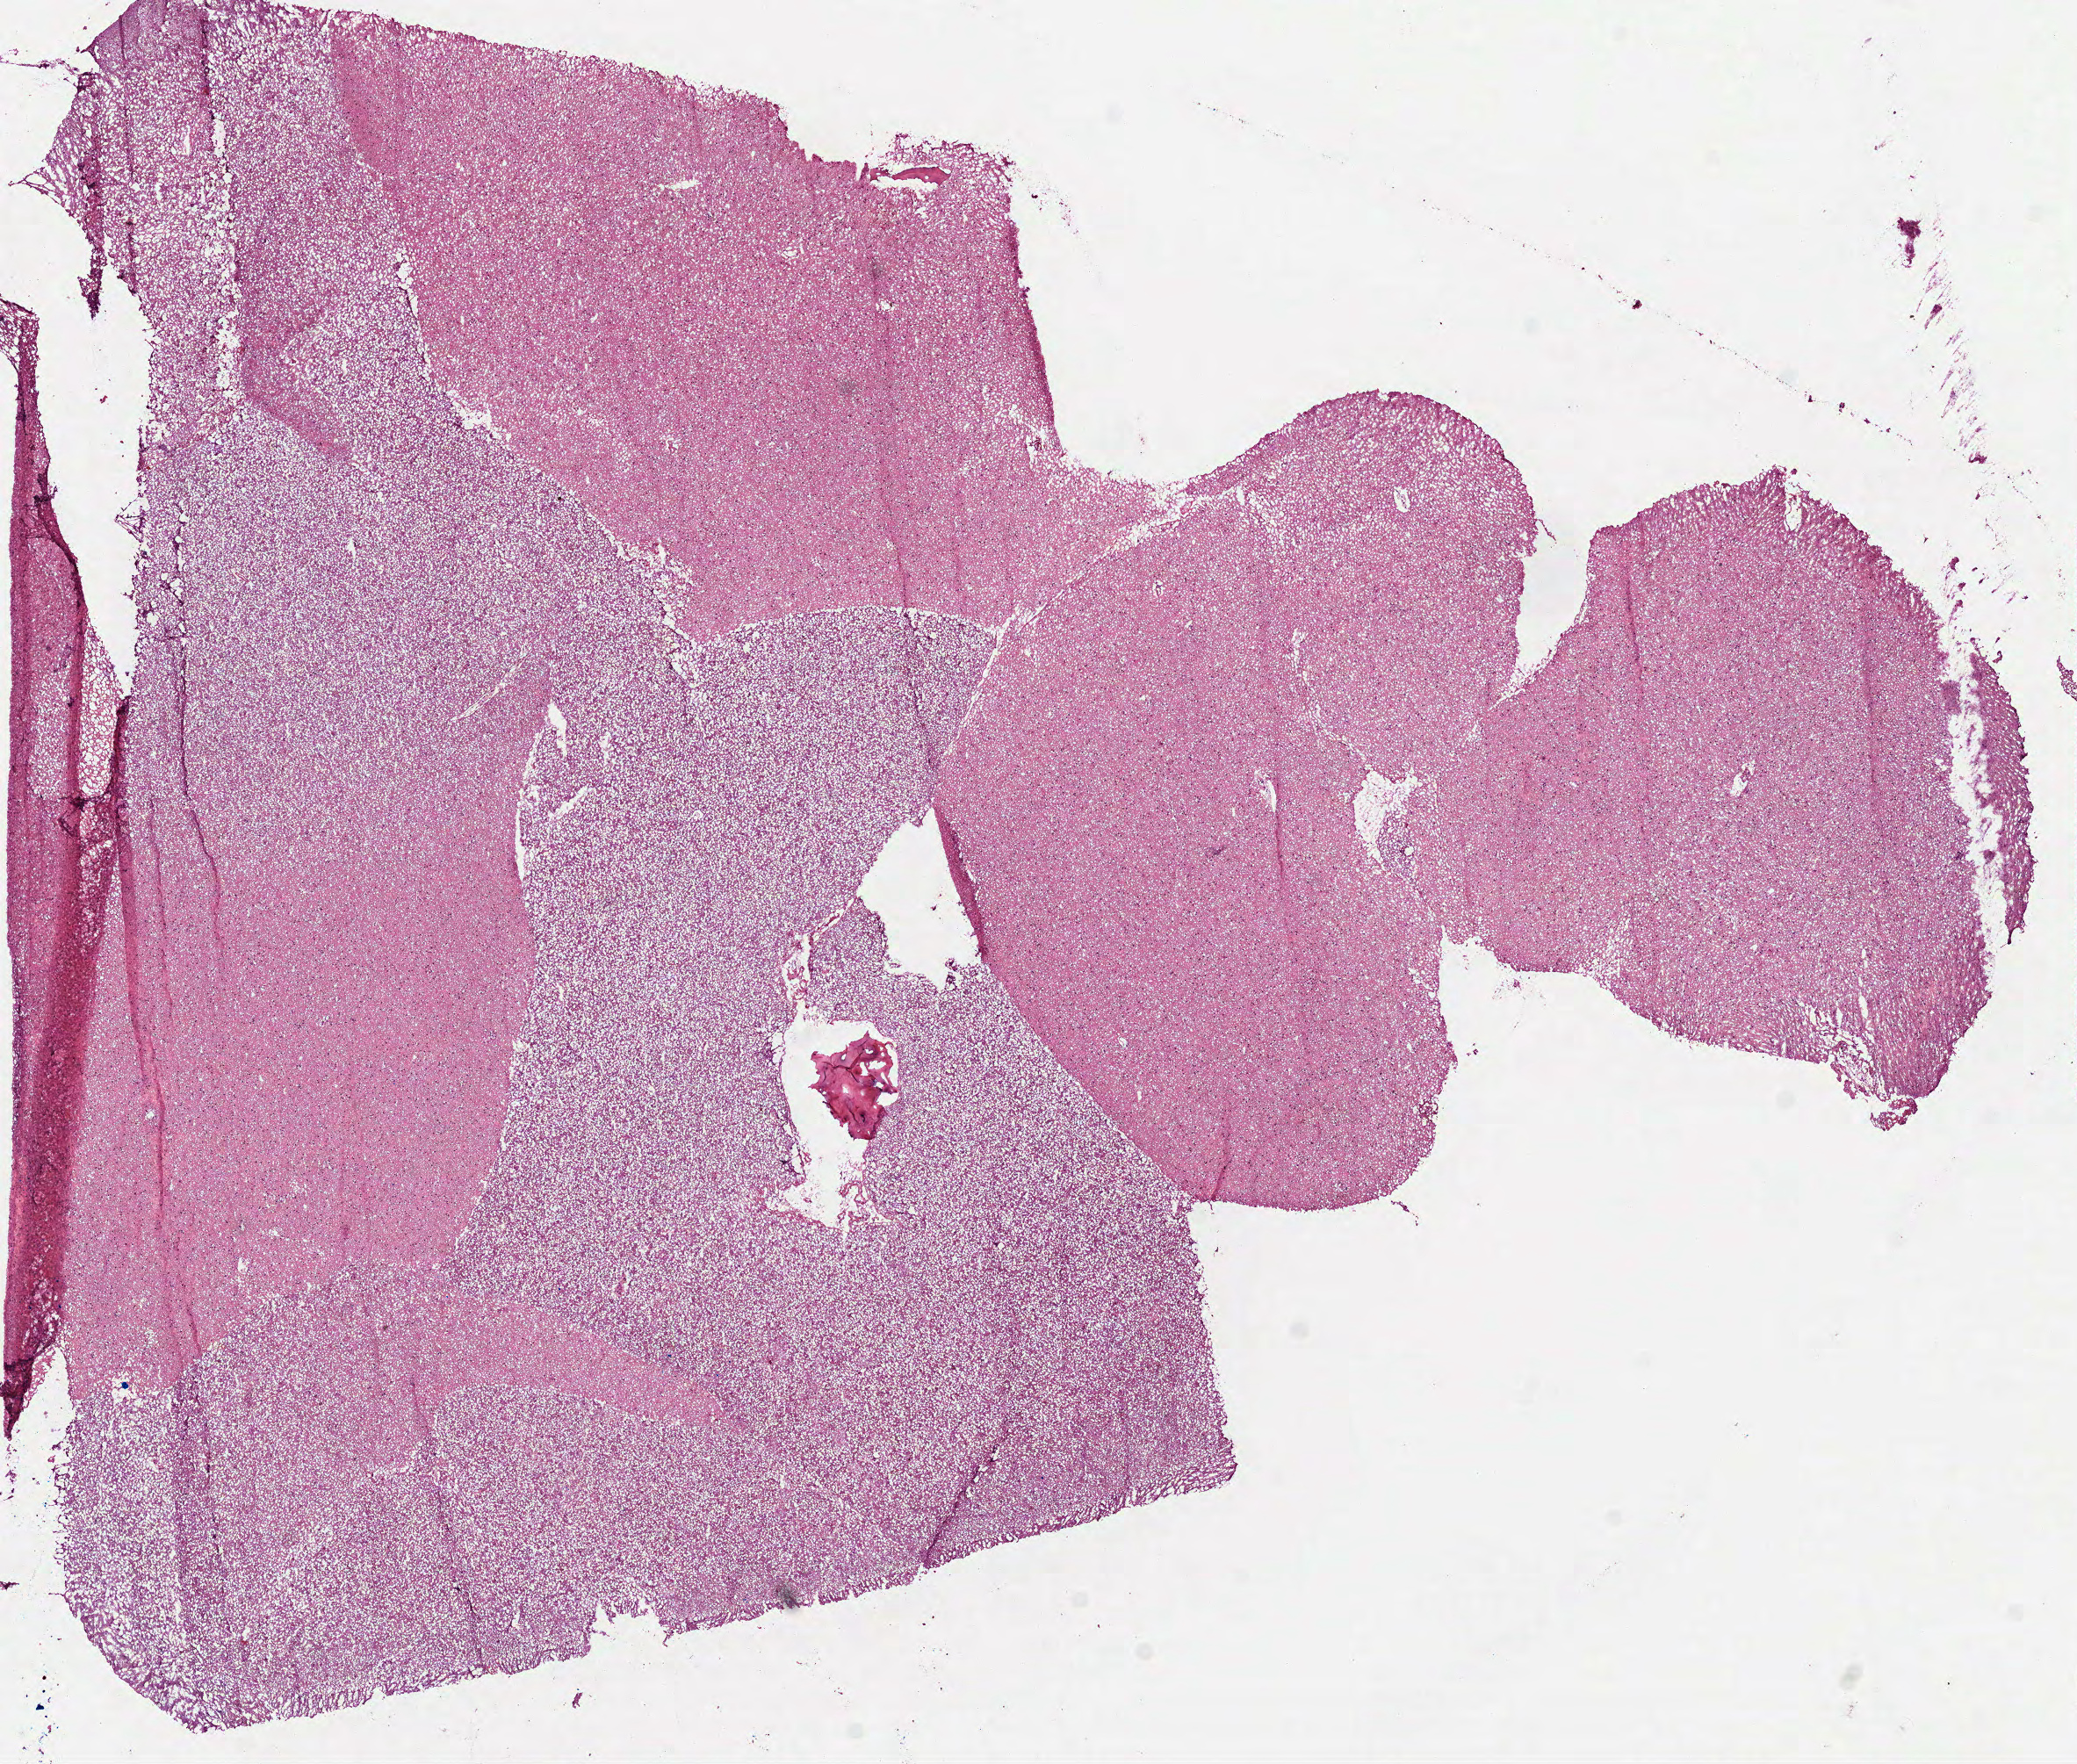
Digitized H&E tissue section (whole slide) — shown as a low-resolution overview of the whole scanned area (about 9.5 x 8.1 mm), frozen section from the top of the tissue portion, brain, solid tissue normal (non-tumour tissue) sample. Male patient; age at initial diagnosis 67 years.
This section: solid tissue normal (non-tumour) sample from the same patient. Patient diagnosis: Glioblastoma.